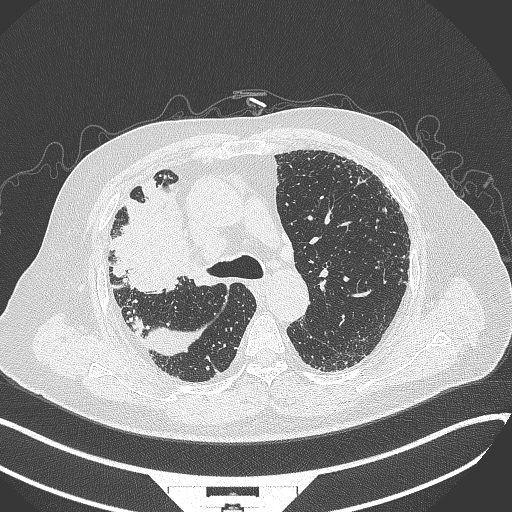
Chest CT, one axial slice; position 235 of 384 along the scan axis; 120 kVp; lung window (W 1500 / L -600 HU); 1 mm slice thickness; 512 × 512 image matrix, field of view 400 × 400 mm. Male patient, age 69 years. From the clinical record (not read from this slice): clinical TNM (as recorded): T4 N3 M1.
Annotated regions visible in this slice (rectangle marked by the reading radiologist):
- lung tumour (recorded histology: adenocarcinoma): bounding box <104,184,190,298> (left, top, right, bottom; pixels)